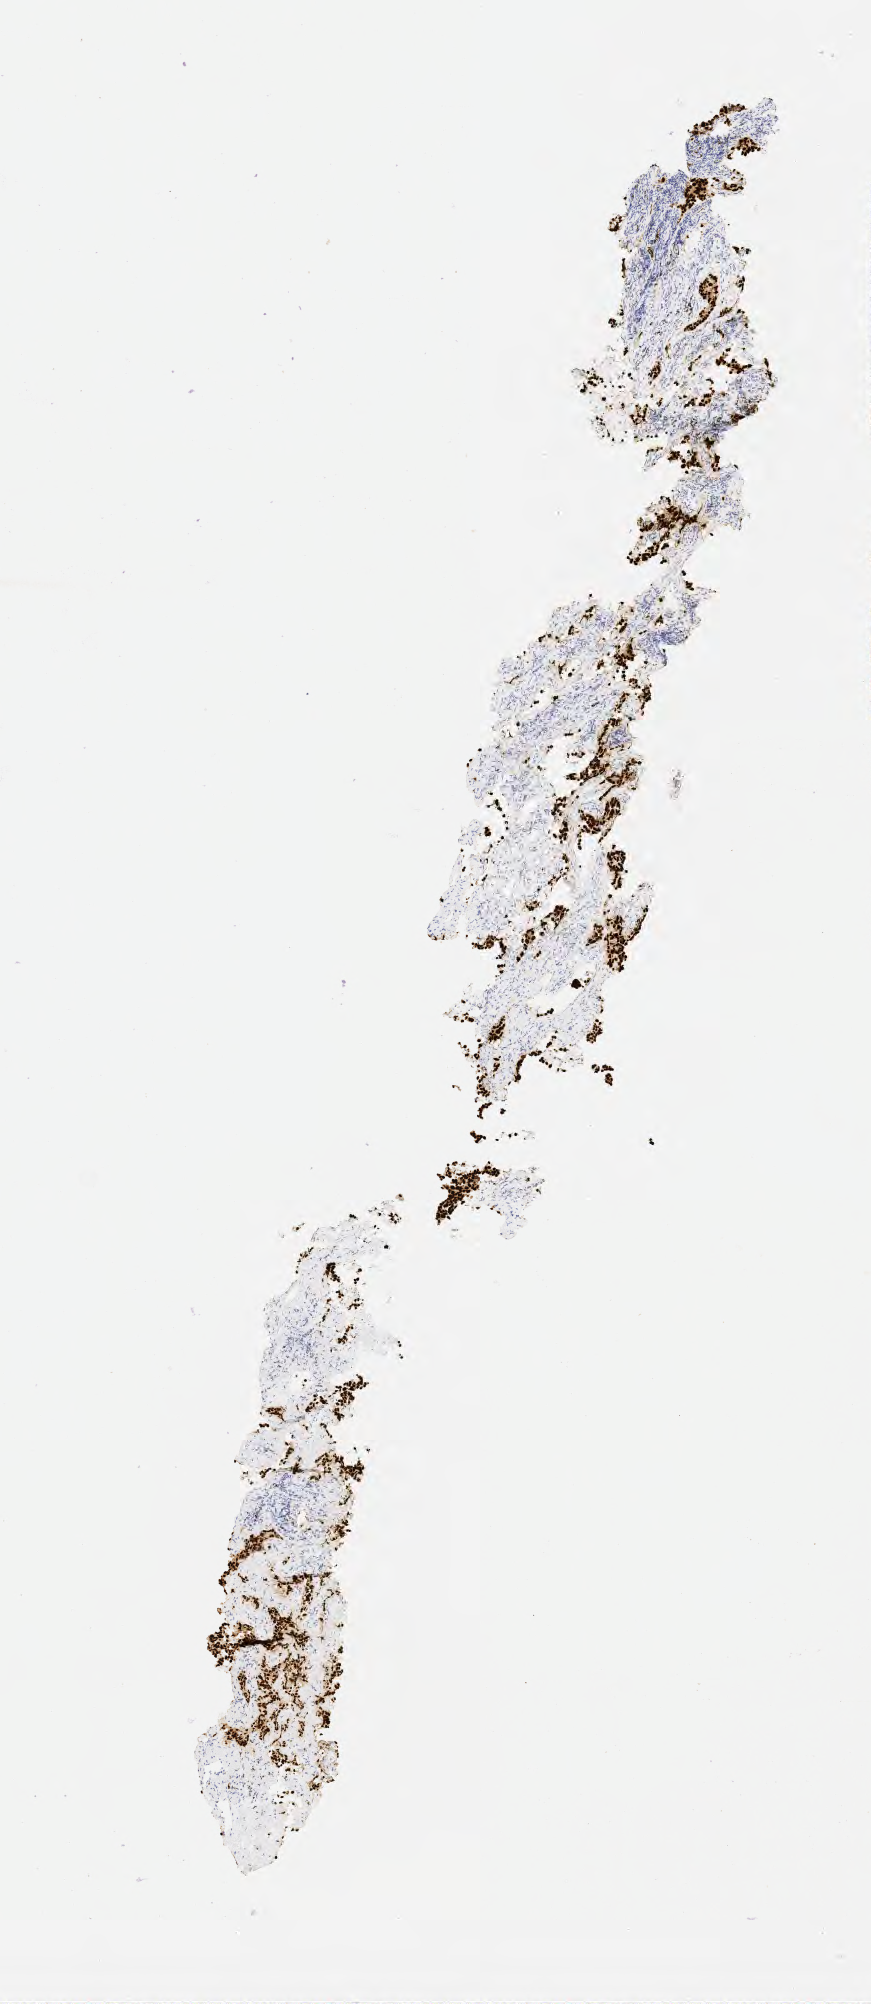
Immunohistochemistry (IHC) whole-slide image stained for TTF-1 (thyroid transcription factor 1), whole scanned area (about 3.5 x 8.1 mm) shown as a low-resolution overview. Tumor tissue. Anatomic site: lung. Patient: male, 67 years old.
Histologic diagnosis: Adenocarcinoma, NOS.